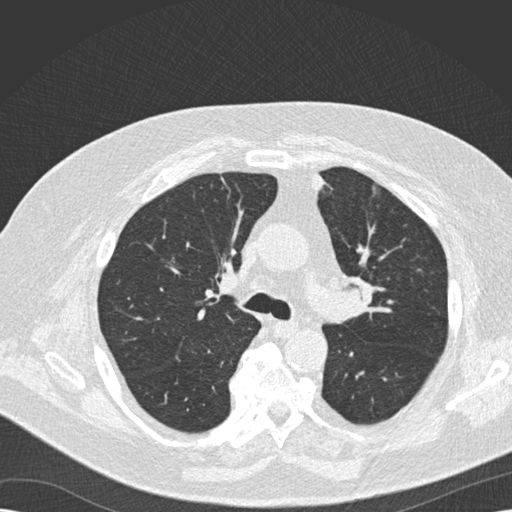
Low-dose screening chest CT, one axial slice. Slice 111 of 173 in the series (ordered by position). Reconstruction kernel B30f. 120 kVp. Lung window (W 1500 / L -600 HU). 2 mm slice thickness. 512 × 512 image matrix, field of view 370 × 370 mm.
Annotated regions visible in this slice (manually delineated by an expert):
- lesion 1 (tumor, upper lobe of left lung): bounding box [x1, y1, x2, y2] px = [314, 173, 324, 189]